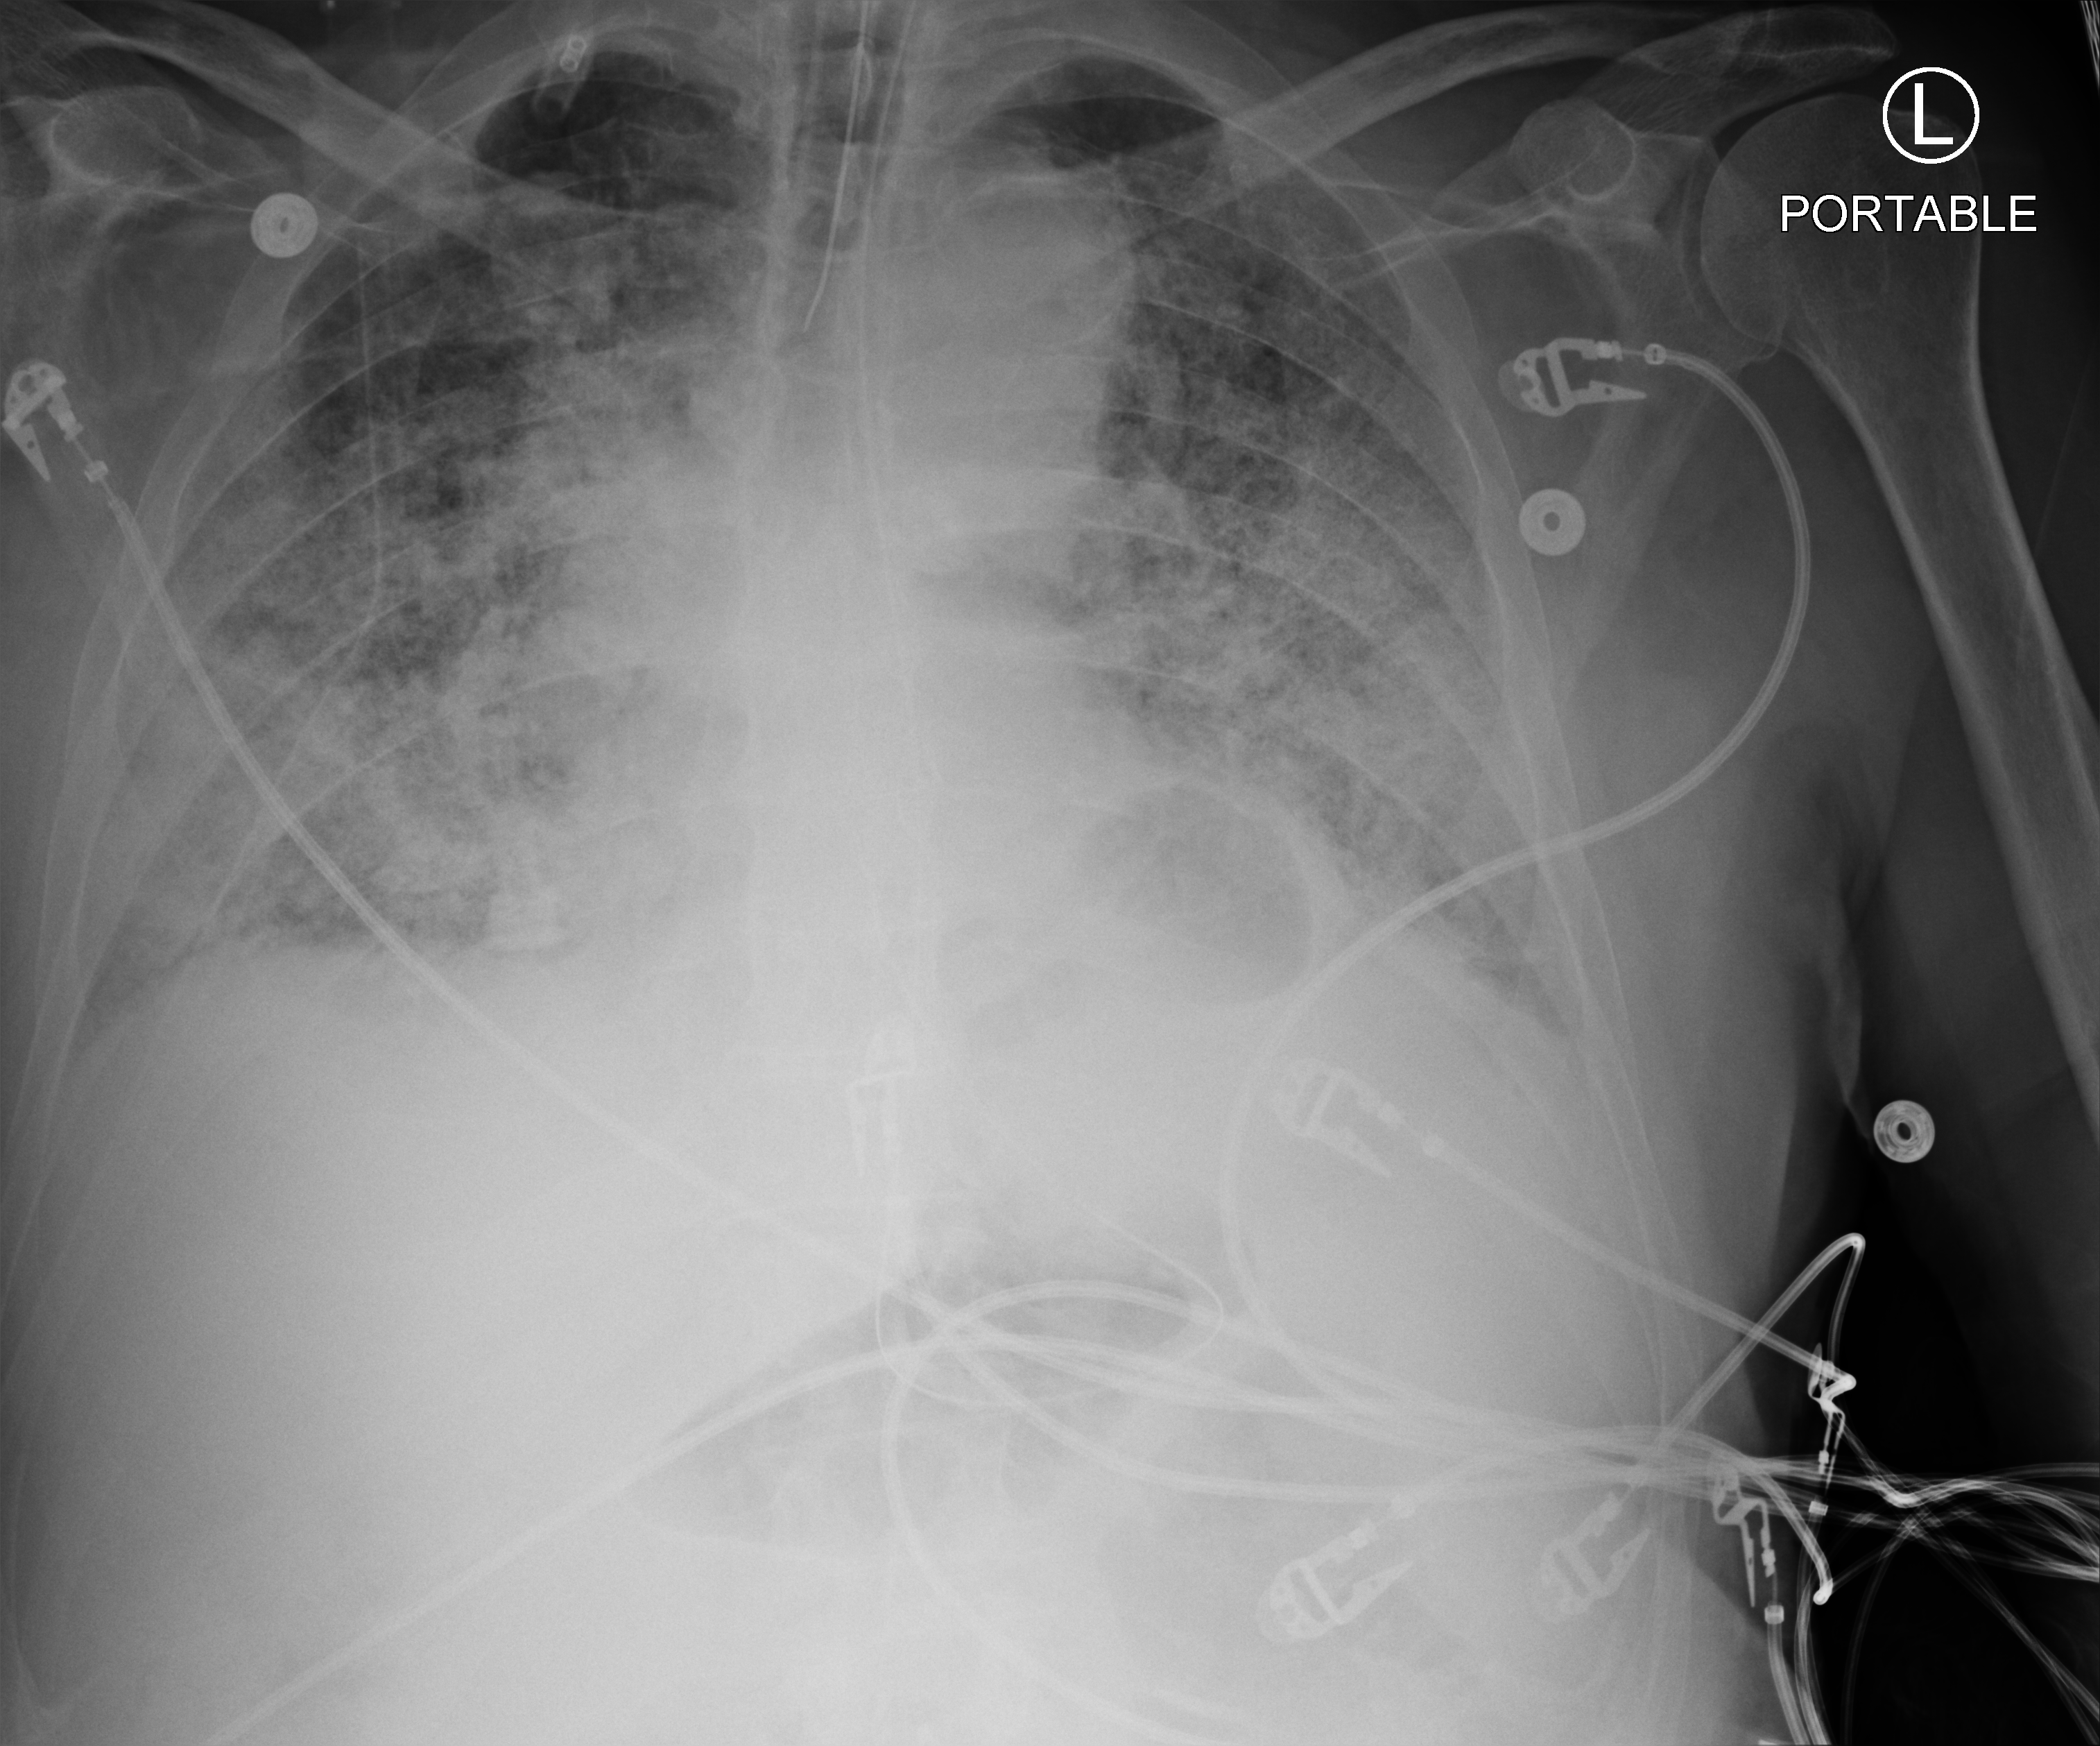
Bedside chest radiograph (computed radiography); anteroposterior (AP) projection. Male patient hospitalised with COVID-19, age 75–90 years.
From the hospital-stay record, not from the radiograph (when in the stay this image was taken is not recorded): other chronic lung disease (admission record): no; admitted to intensive care during this hospital stay: yes; diabetes (admission record): no.